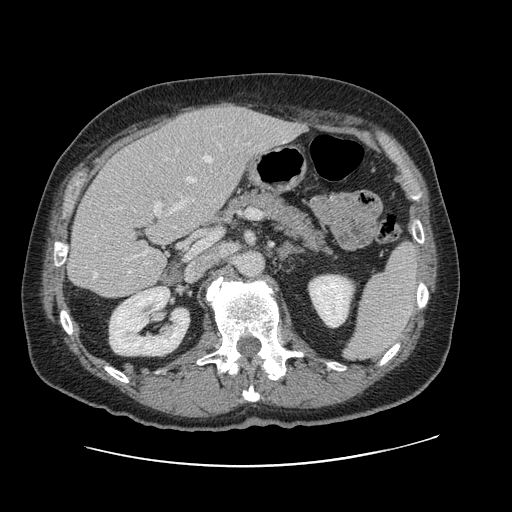
Contrast-enhanced abdominal CT, one axial slice; slice 57 of 138 in the series (ordered by position); 120 kVp; intravenous contrast given; soft-tissue window (W 400 / L 40 HU); 2.5 mm slice thickness; 512 × 512 image matrix, field of view 402 × 402 mm. Male patient, age 71 years. Case-level facts recorded for this patient, not image findings: diagnosis: colorectal cancer liver metastases, imaged before liver resection; multiple liver metastases: no; largest metastasis: 3.3 cm.
Structures marked on this image (manually delineated by an expert):
- hepatic veins: bounding box <93,156,227,278> (left, top, right, bottom; pixels)
- liver: <70,105,303,297>
- planned liver remnant (the part of the liver to remain after resection): <70,143,202,297>
- portal vein (with intrahepatic branches): <95,199,195,248>